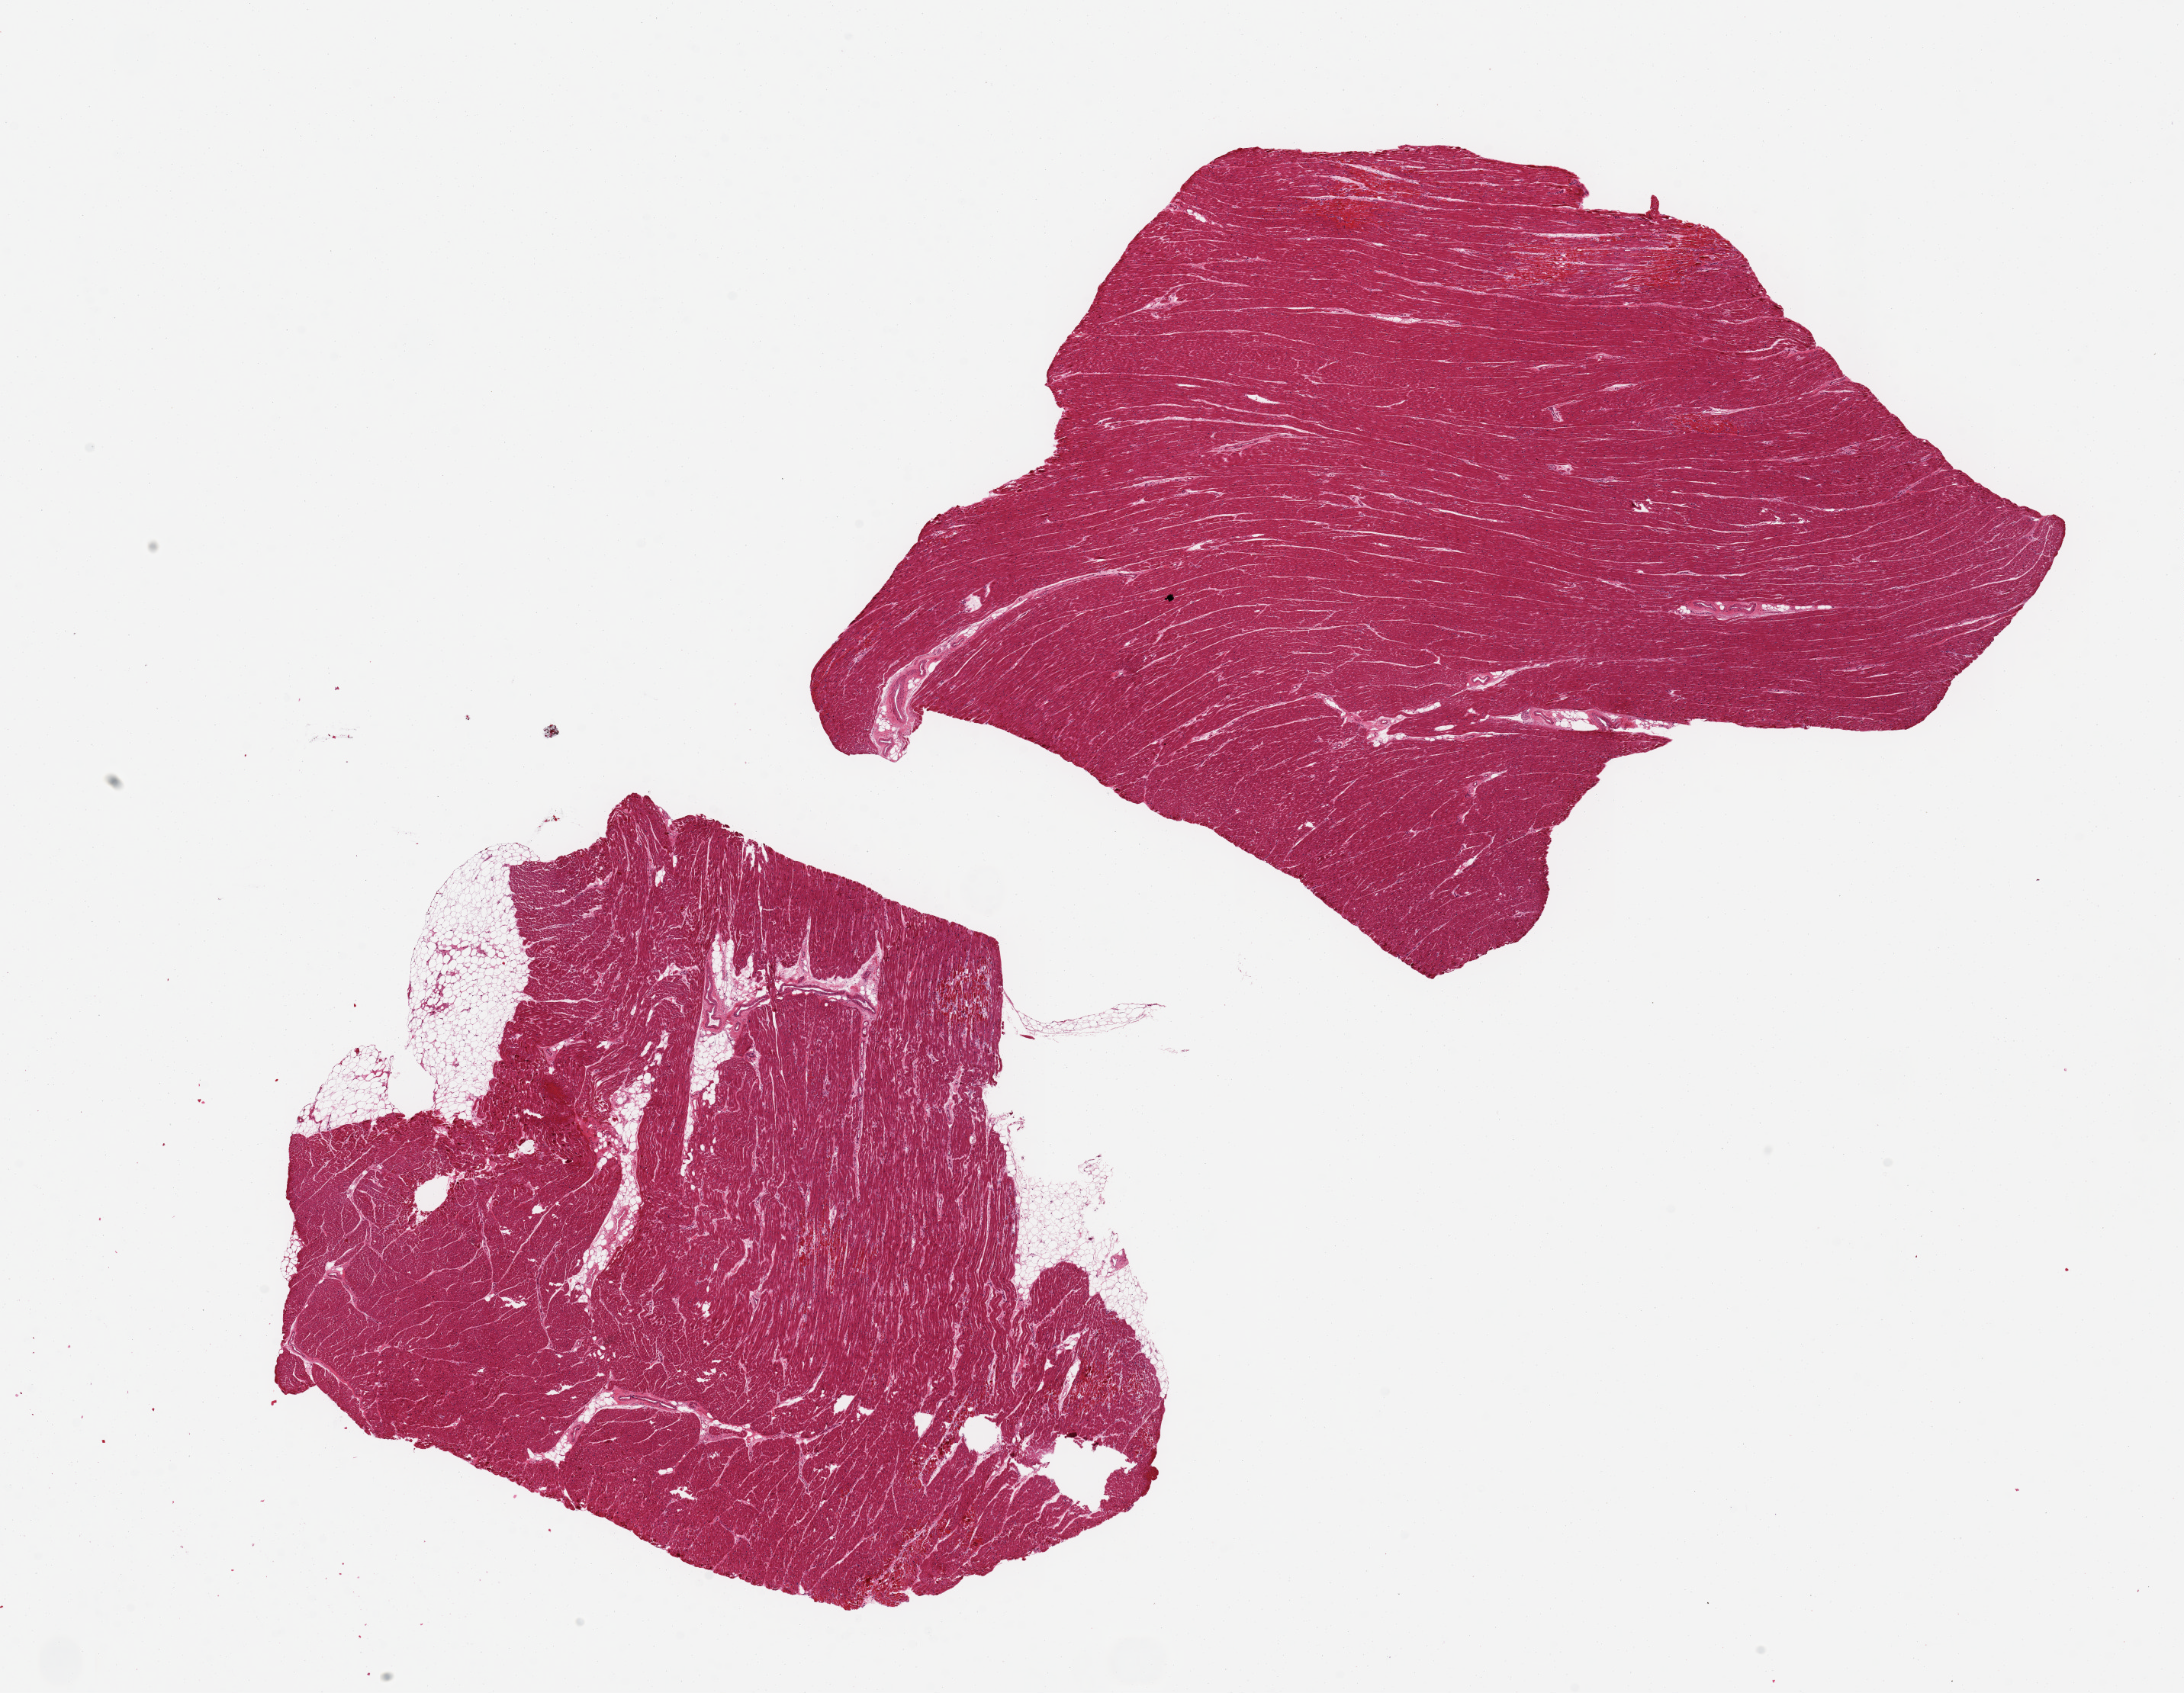
Whole-slide image, hematoxylin and eosin (H&E) stain, brightfield — low-resolution overview of the scanned area, about 22.6 x 17.6 mm (acquisition: 20x scan), PAXgene-fixed paraffin-embedded (PFPE) section, section of heart (target tissue), donor tissue sample. Donor: male.
Review note (as recorded): 2 pieces, 9x7 & 9x7 mm; 1 has ~10% adipose.